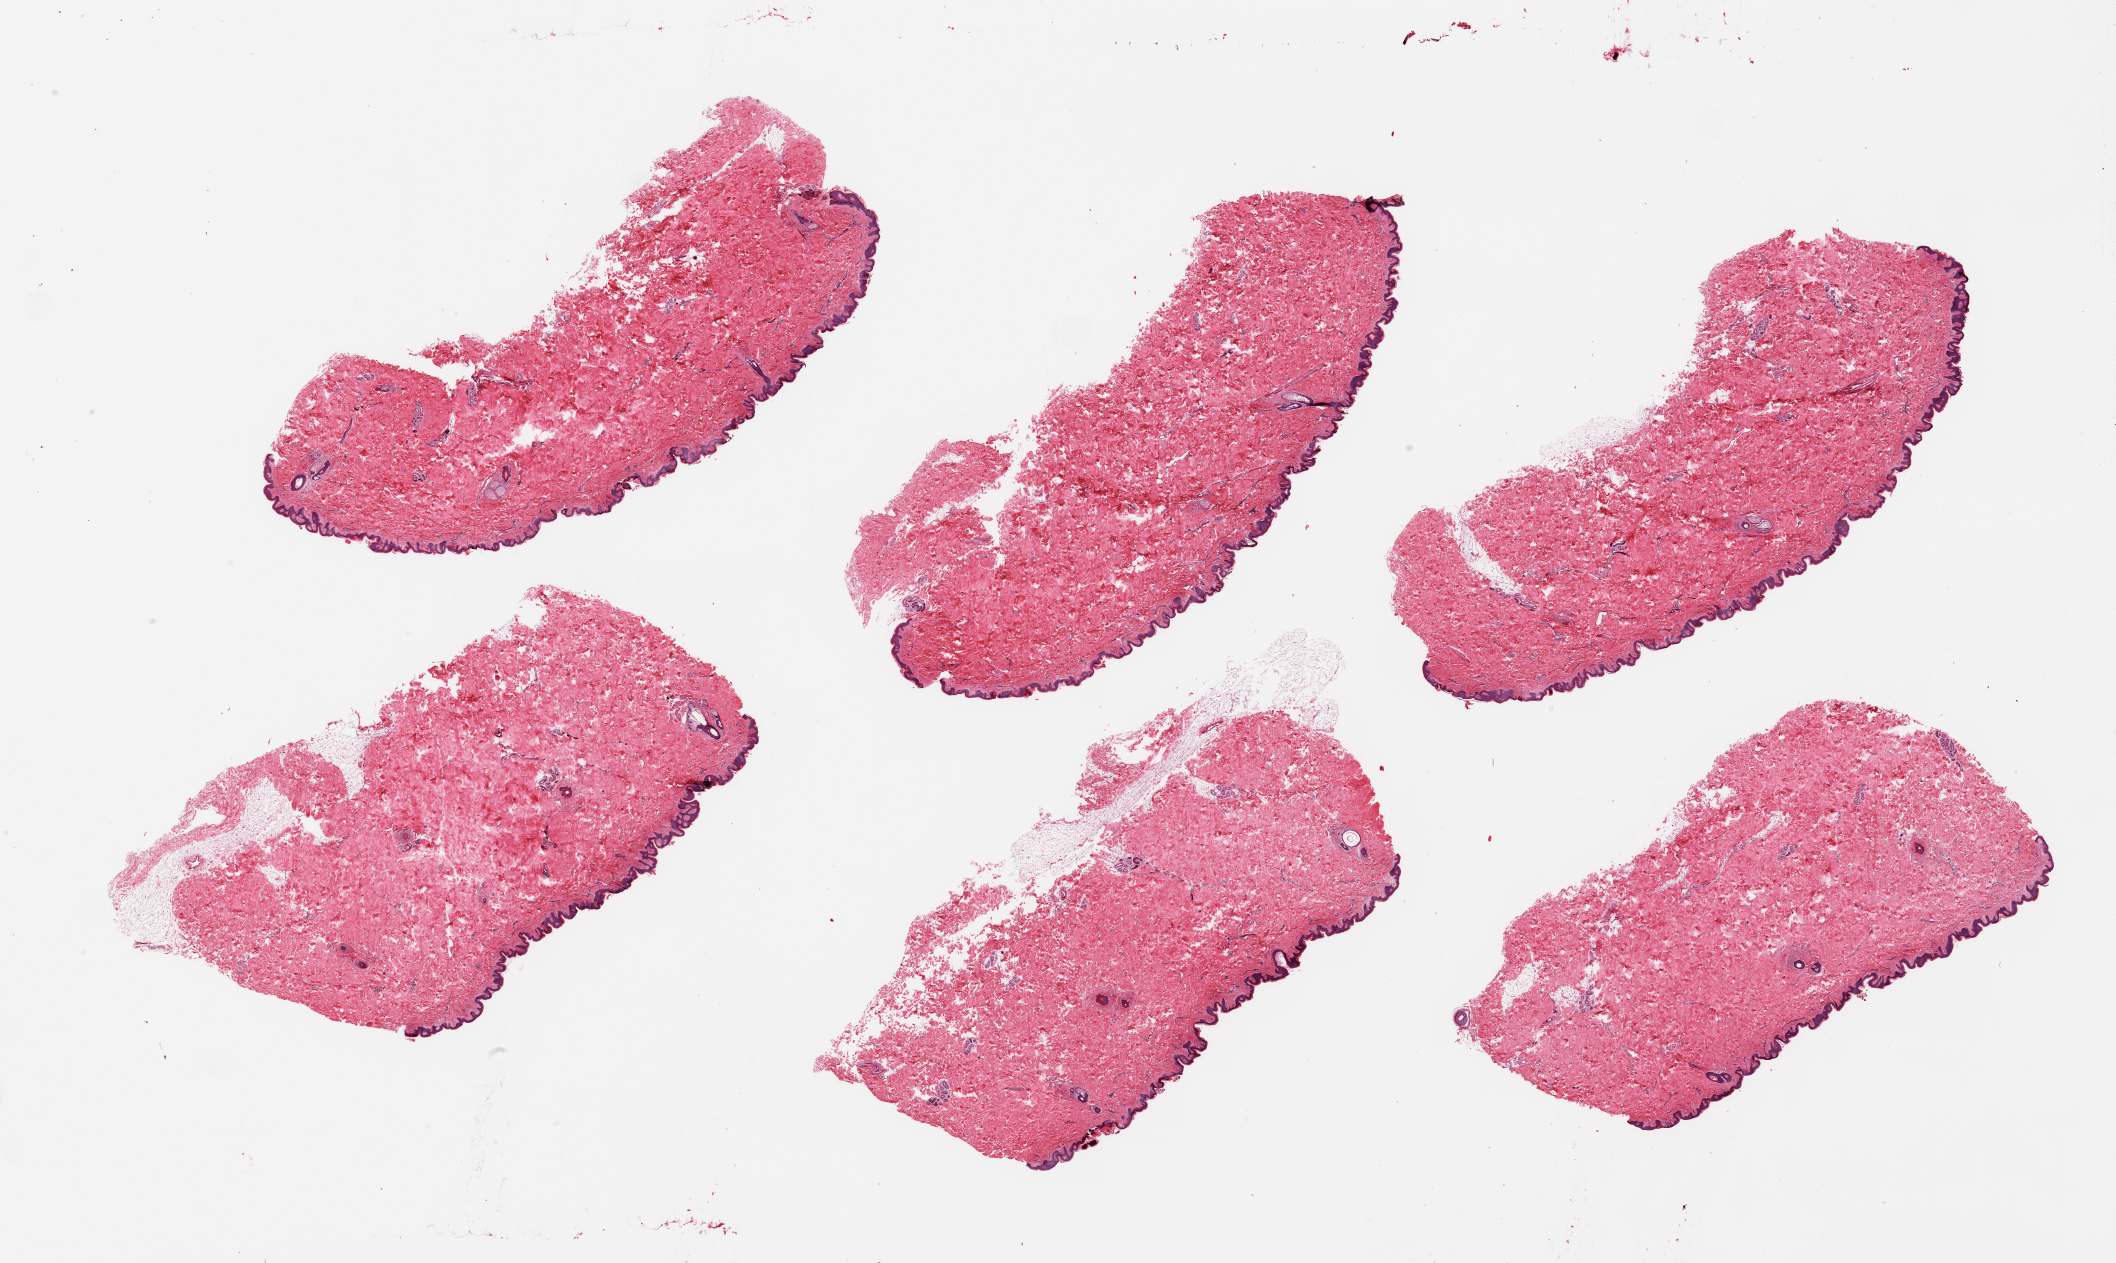
Hematoxylin and eosin (H&E) whole-slide image, low-resolution overview of the scanned area, about 33.5 x 20.0 mm. PAXgene-fixed, paraffin-embedded tissue. Section of skin of suprapubic region (target tissue). Tissue donor sample. Donor sex: male.
Pathologist's review note for this sample: 6 pieces, no dermal fat; squamous epithelium is ~80 microns.